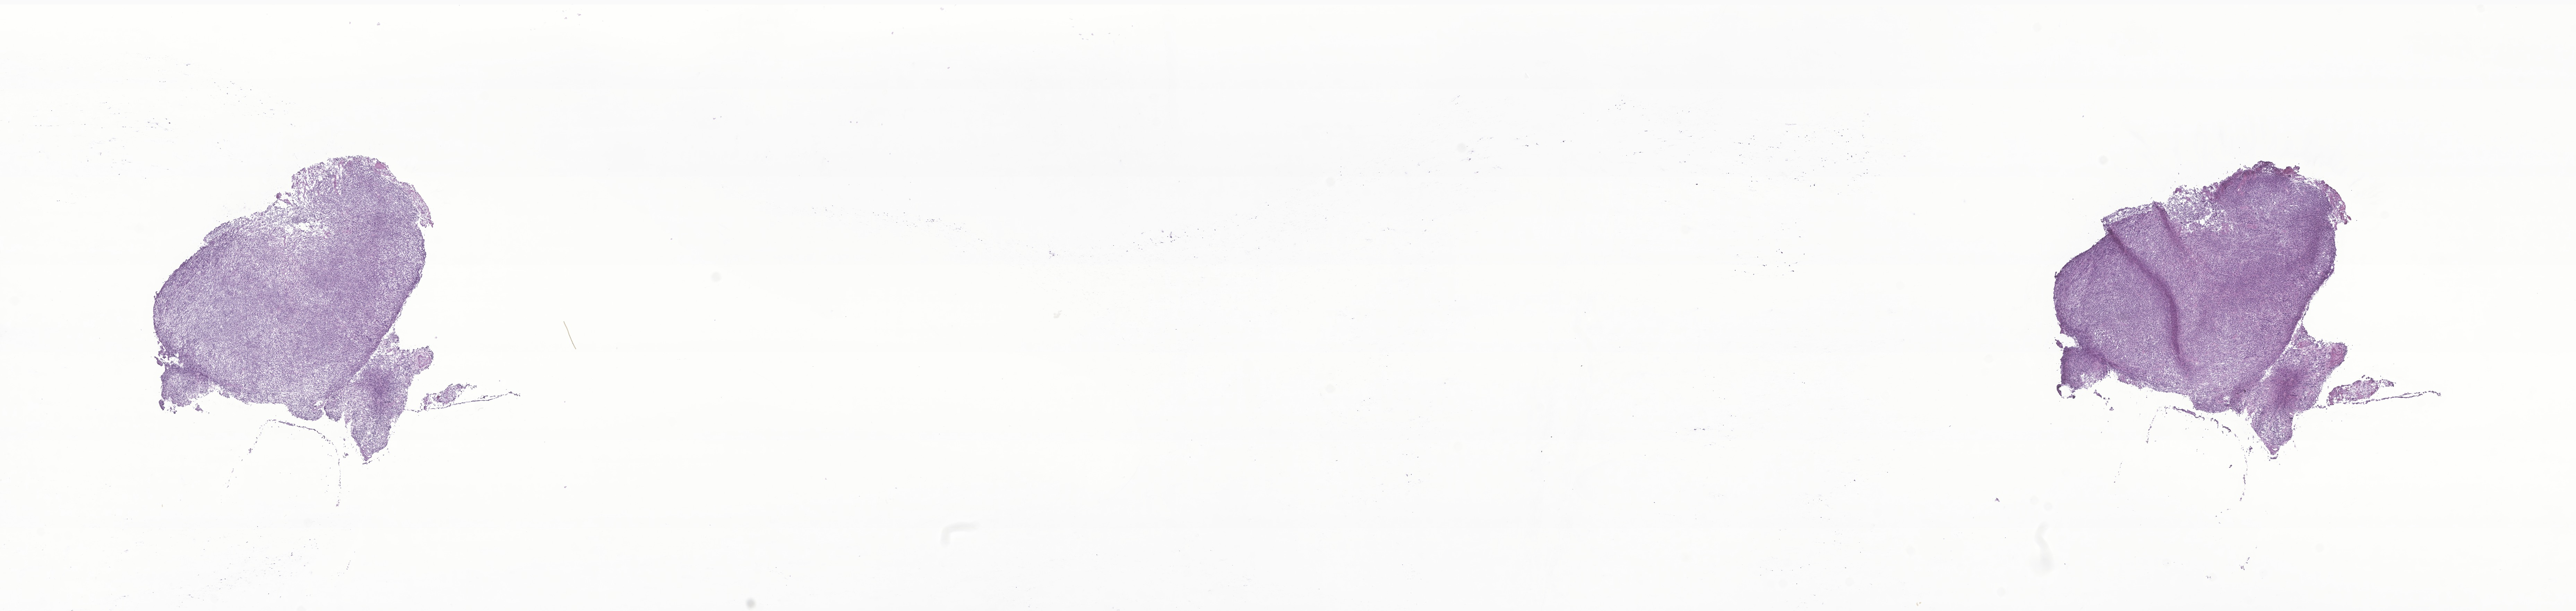
Whole-slide image, hematoxylin and eosin (H&E) stain of tumor tissue from the brain — low-resolution overview of the scanned area, about 31.3 x 7.4 mm. Cryosection (OCT / tissue freezing medium). Female patient, age 609 days (about 1.7 years).
• diagnosis: Desmoplastic nodular medulloblastoma